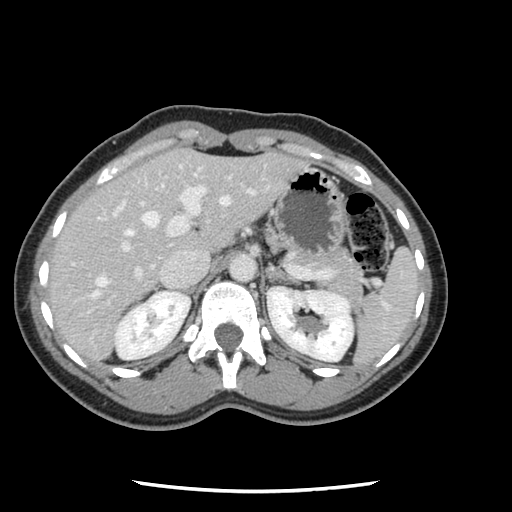
Contrast-enhanced abdominal CT, one axial slice. Position 79 of 134 along the scan axis. 120 kVp. Intravenous contrast given. Soft-tissue window (W 400 / L 40 HU). 2.5 mm slice thickness. 512 × 512 image matrix. Female patient, age 43 years. From the clinical record (not read from this slice): diagnosis: colorectal cancer liver metastases, imaged before liver resection; multiple liver metastases: yes; largest metastasis: 3.4 cm; disease in both lobes: yes.
Annotated regions visible in this slice (manually delineated by an expert):
- hepatic veins: bounding box (x1, y1, x2, y2) in pixels: (91, 173, 231, 299)
- liver: (48, 150, 301, 362)
- planned liver remnant (the part of the liver to remain after resection): (48, 154, 189, 305)
- portal vein (with intrahepatic branches): (87, 165, 256, 314)